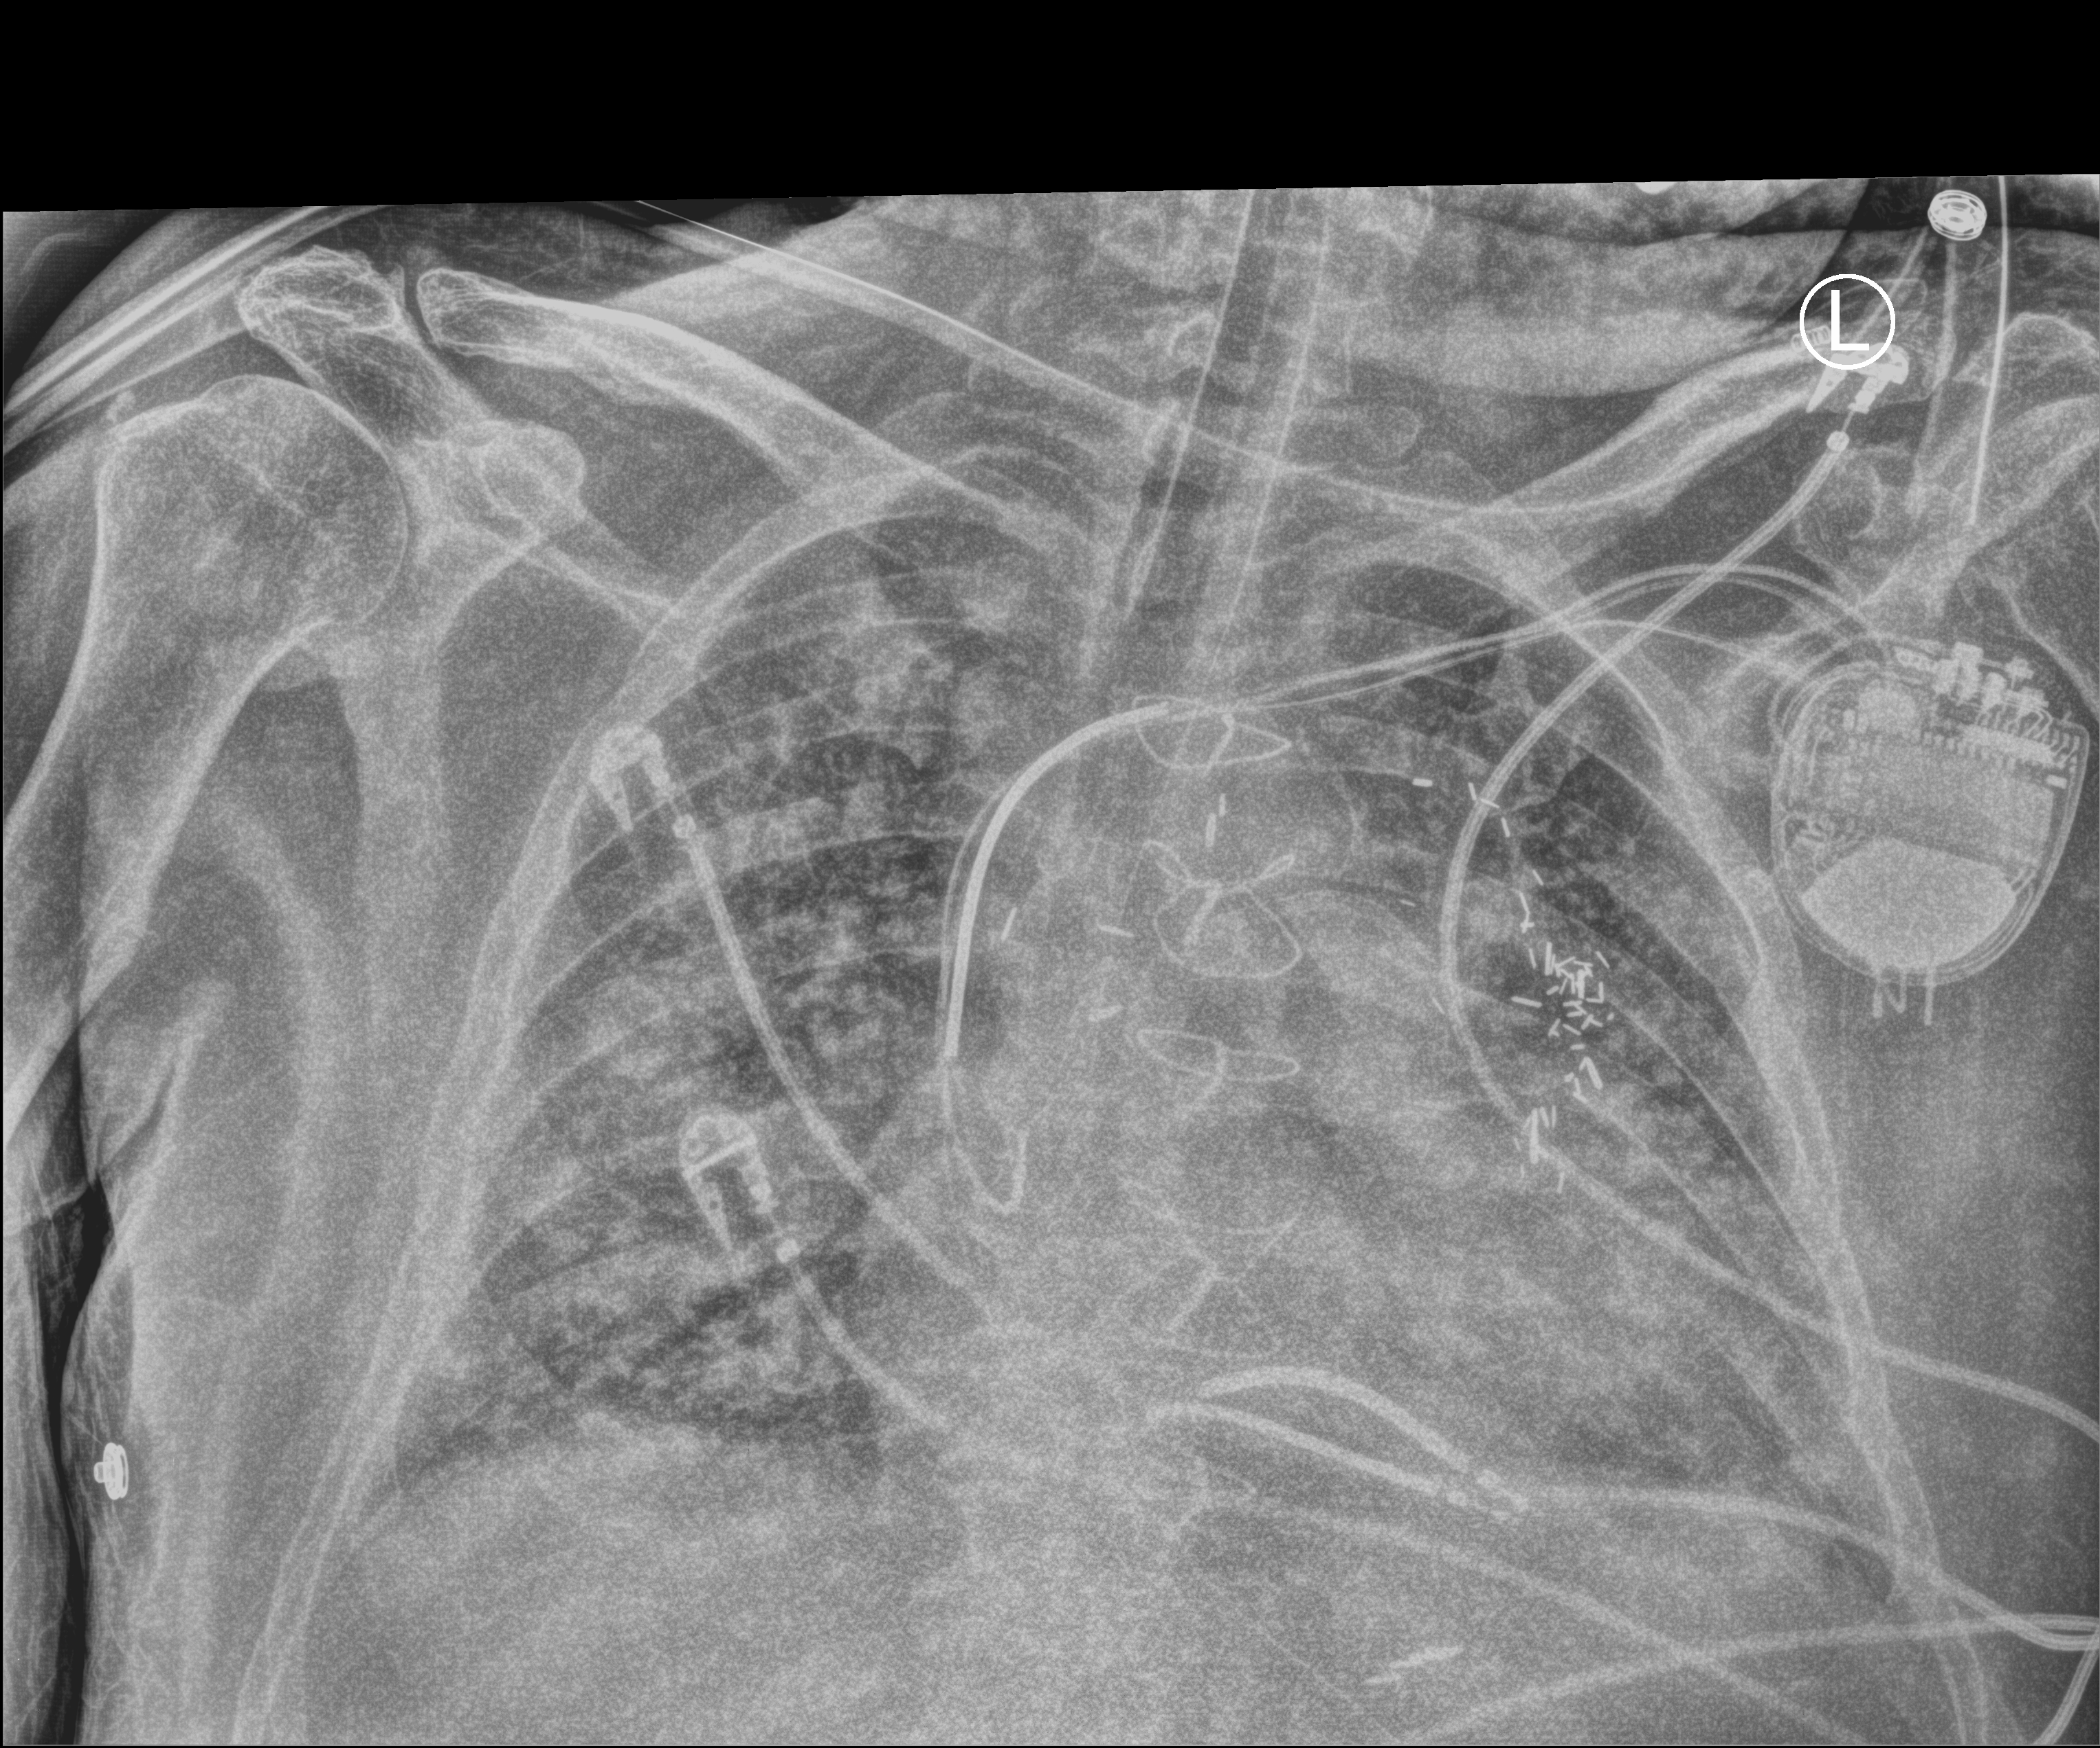
Chest X-ray (portable); anteroposterior (AP) projection. Male patient hospitalised with COVID-19, age 60–74 years.
Hospital-stay facts (about this admission, not read from this image; timing relative to this image not recorded):
- length of hospital stay: 55 days